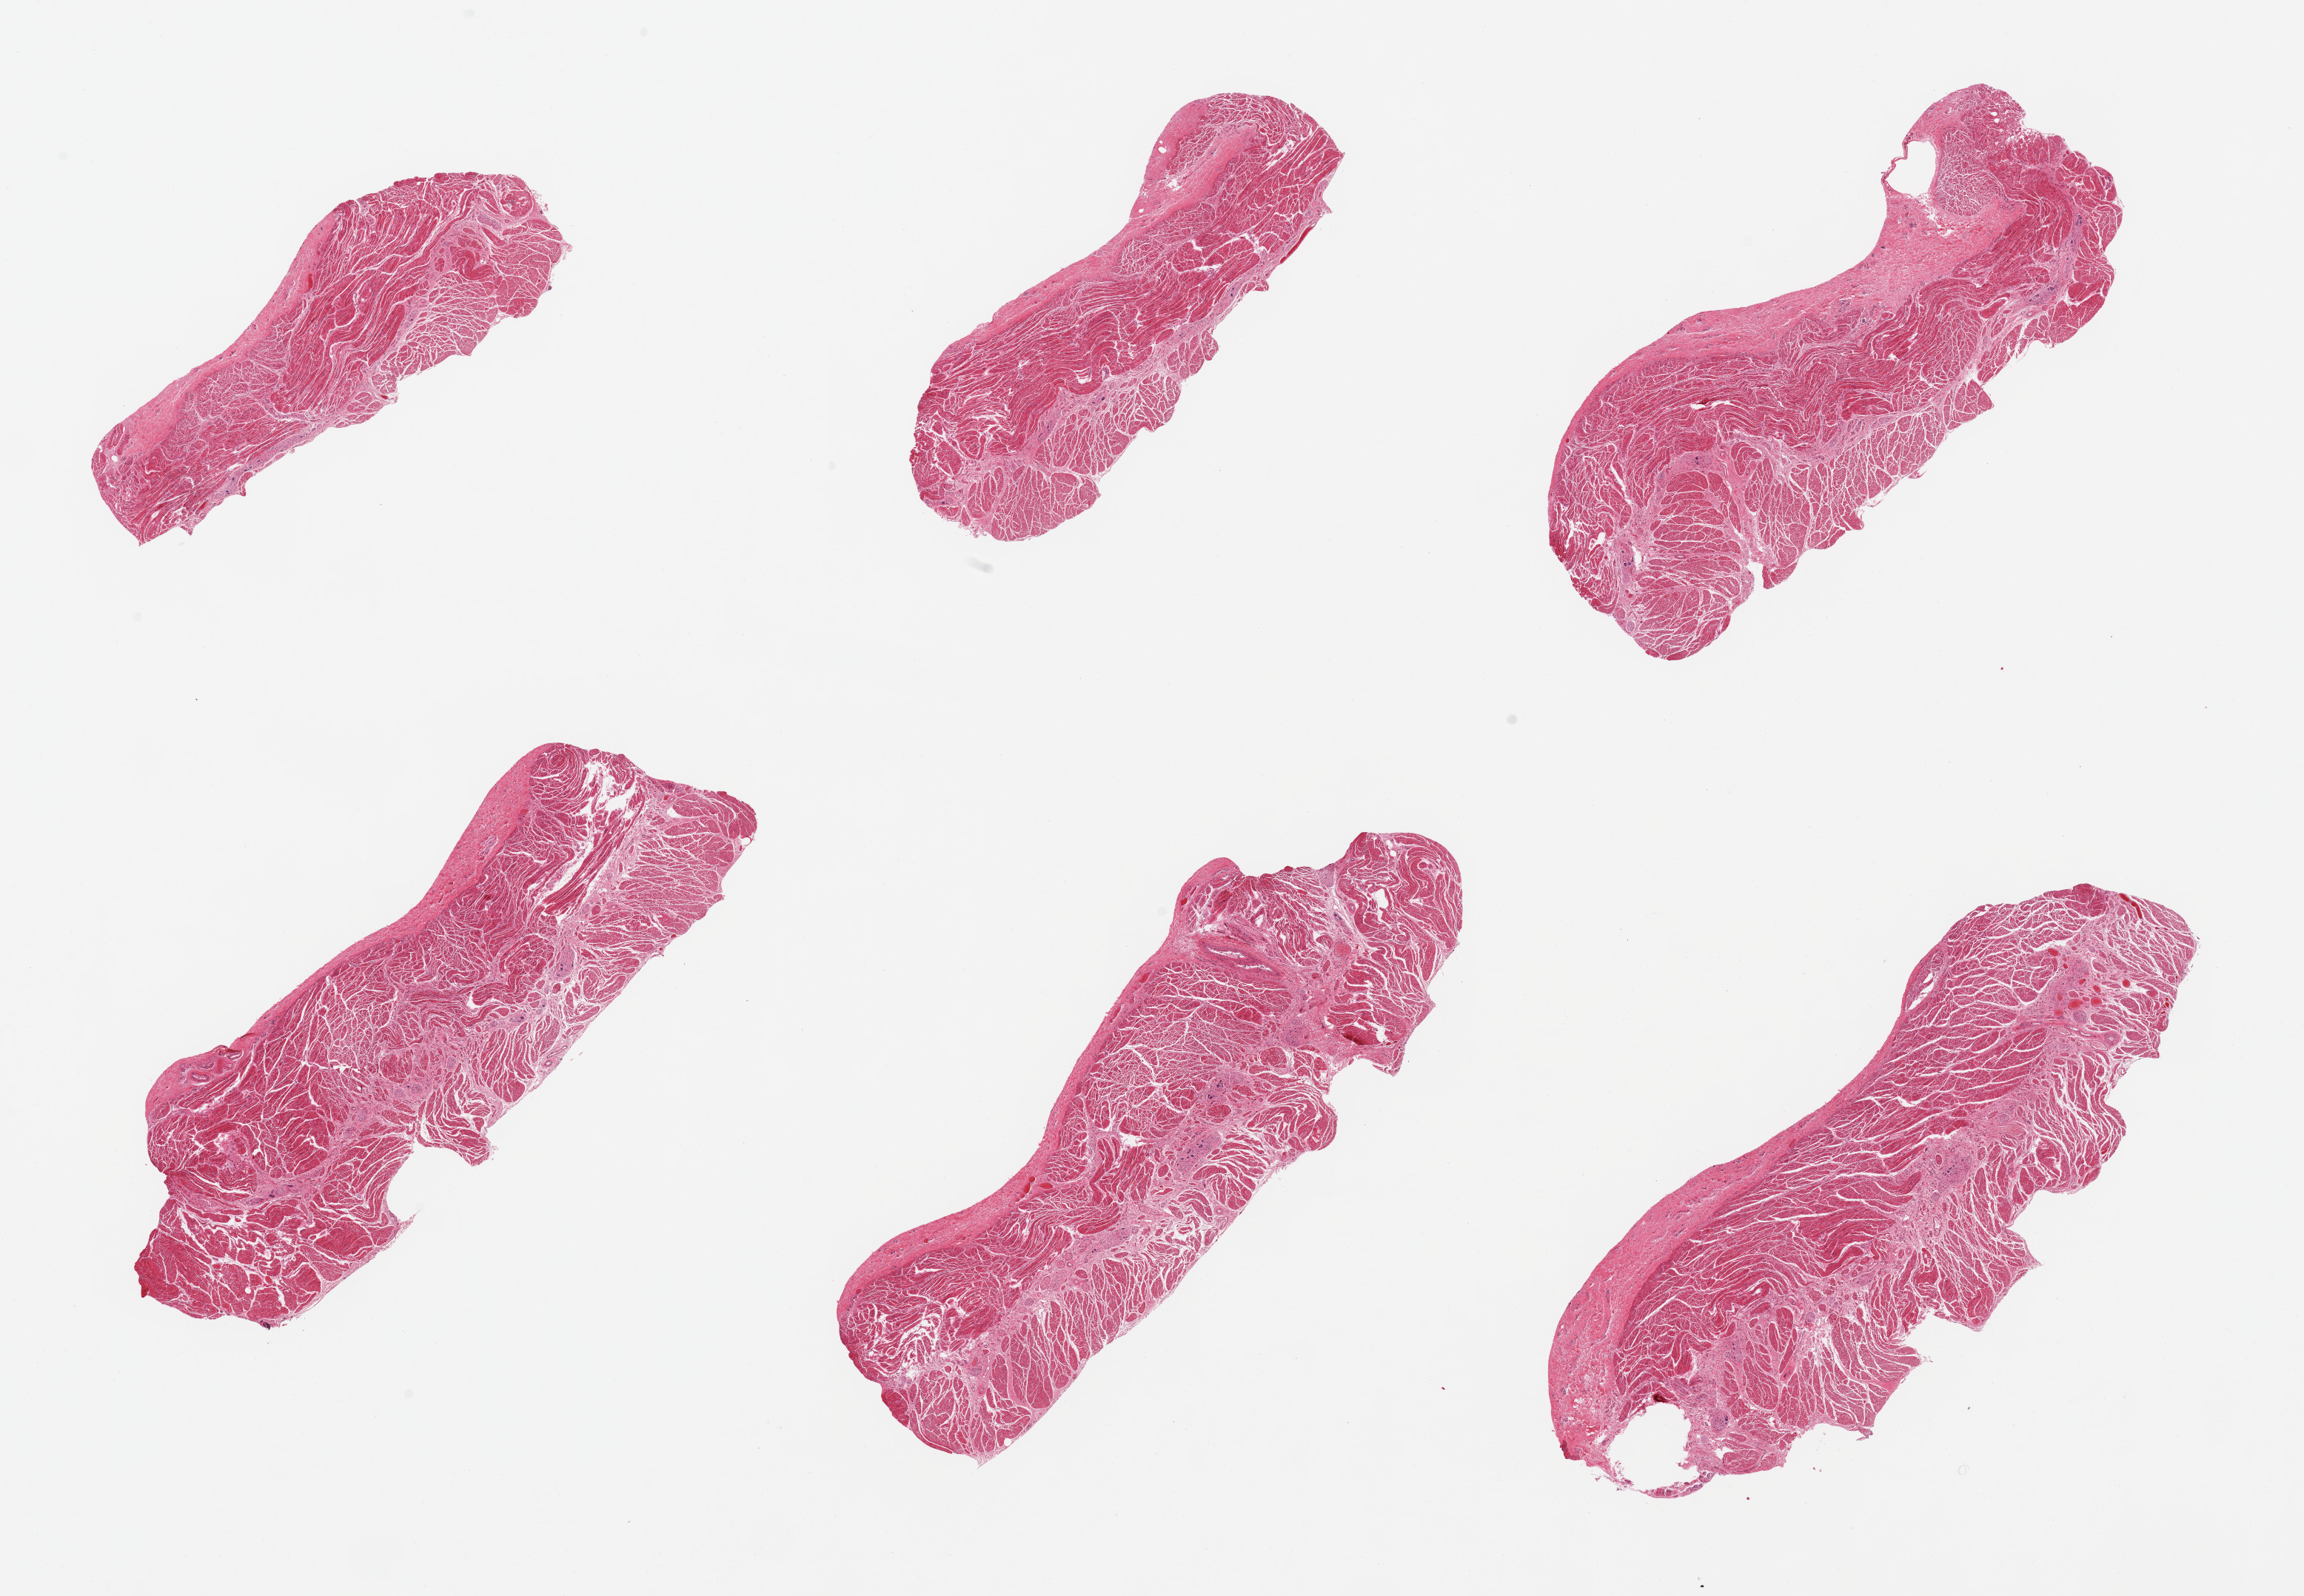
Whole-slide image, H&E stain — shown as a low-resolution overview of the whole scanned area (about 24.6 x 17.1 mm, acquisition: 20x scan), PAXgene-fixed paraffin-embedded (PFPE) section, section of esophageal muscle (target tissue), donor tissue sample. Donor sex: female.
Pathologist's review note for this sample: 6 pieces; well trimmed.